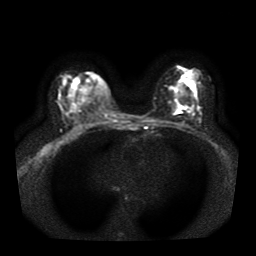
Breast MRI, one axial slice. Diffusion-weighted series; image 2 of 4 stored at this slice position (different b-values; order by instance number). 1.5 T. 5 mm slice thickness. 256 × 256 image matrix, field of view 330 × 330 mm. Female patient.
Structures marked on this image (expert manual segmentation):
- tumour on diffusion-weighted imaging: bounding box [x1, y1, x2, y2] px = [177, 106, 186, 113]